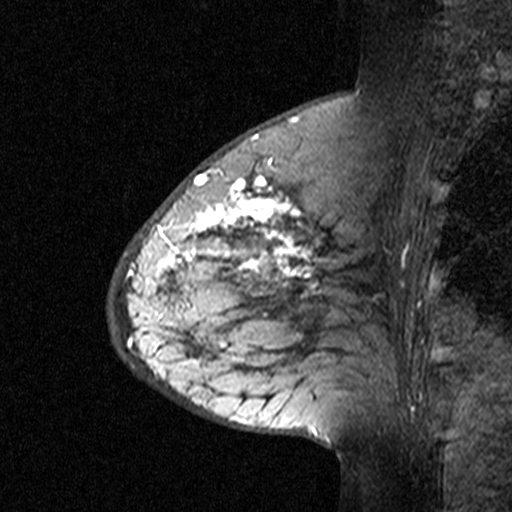
Breast MRI (dynamic contrast-enhanced), one sagittal slice; position 14 of 44 along the scan axis; dynamic contrast-enhanced study with each time point stored as its own series, time point 3 of 4 at this slice position (ordered by acquisition time); 1.5 T; TE 4.5 ms, TR 11 ms; 3 mm slice thickness; 512 × 512 image matrix, field of view 200 × 200 mm. Patient: female, 65 years. From the clinical record (not read from this slice): setting: breast cancer imaged before/during neoadjuvant chemotherapy; receptor status: HER2-positive.
Structures marked on this image (semi-automatic segmentation, software-assisted and operator-edited):
- analysis volume of interest (the breast-tissue region the enhancement analysis was run in; not a lesion): bounding box (x1, y1, x2, y2) in pixels: (182, 190, 353, 361)
- tumour enhancement mask (voxels above the 90 % enhancement threshold inside the analysis volume of interest): (182, 190, 313, 315)